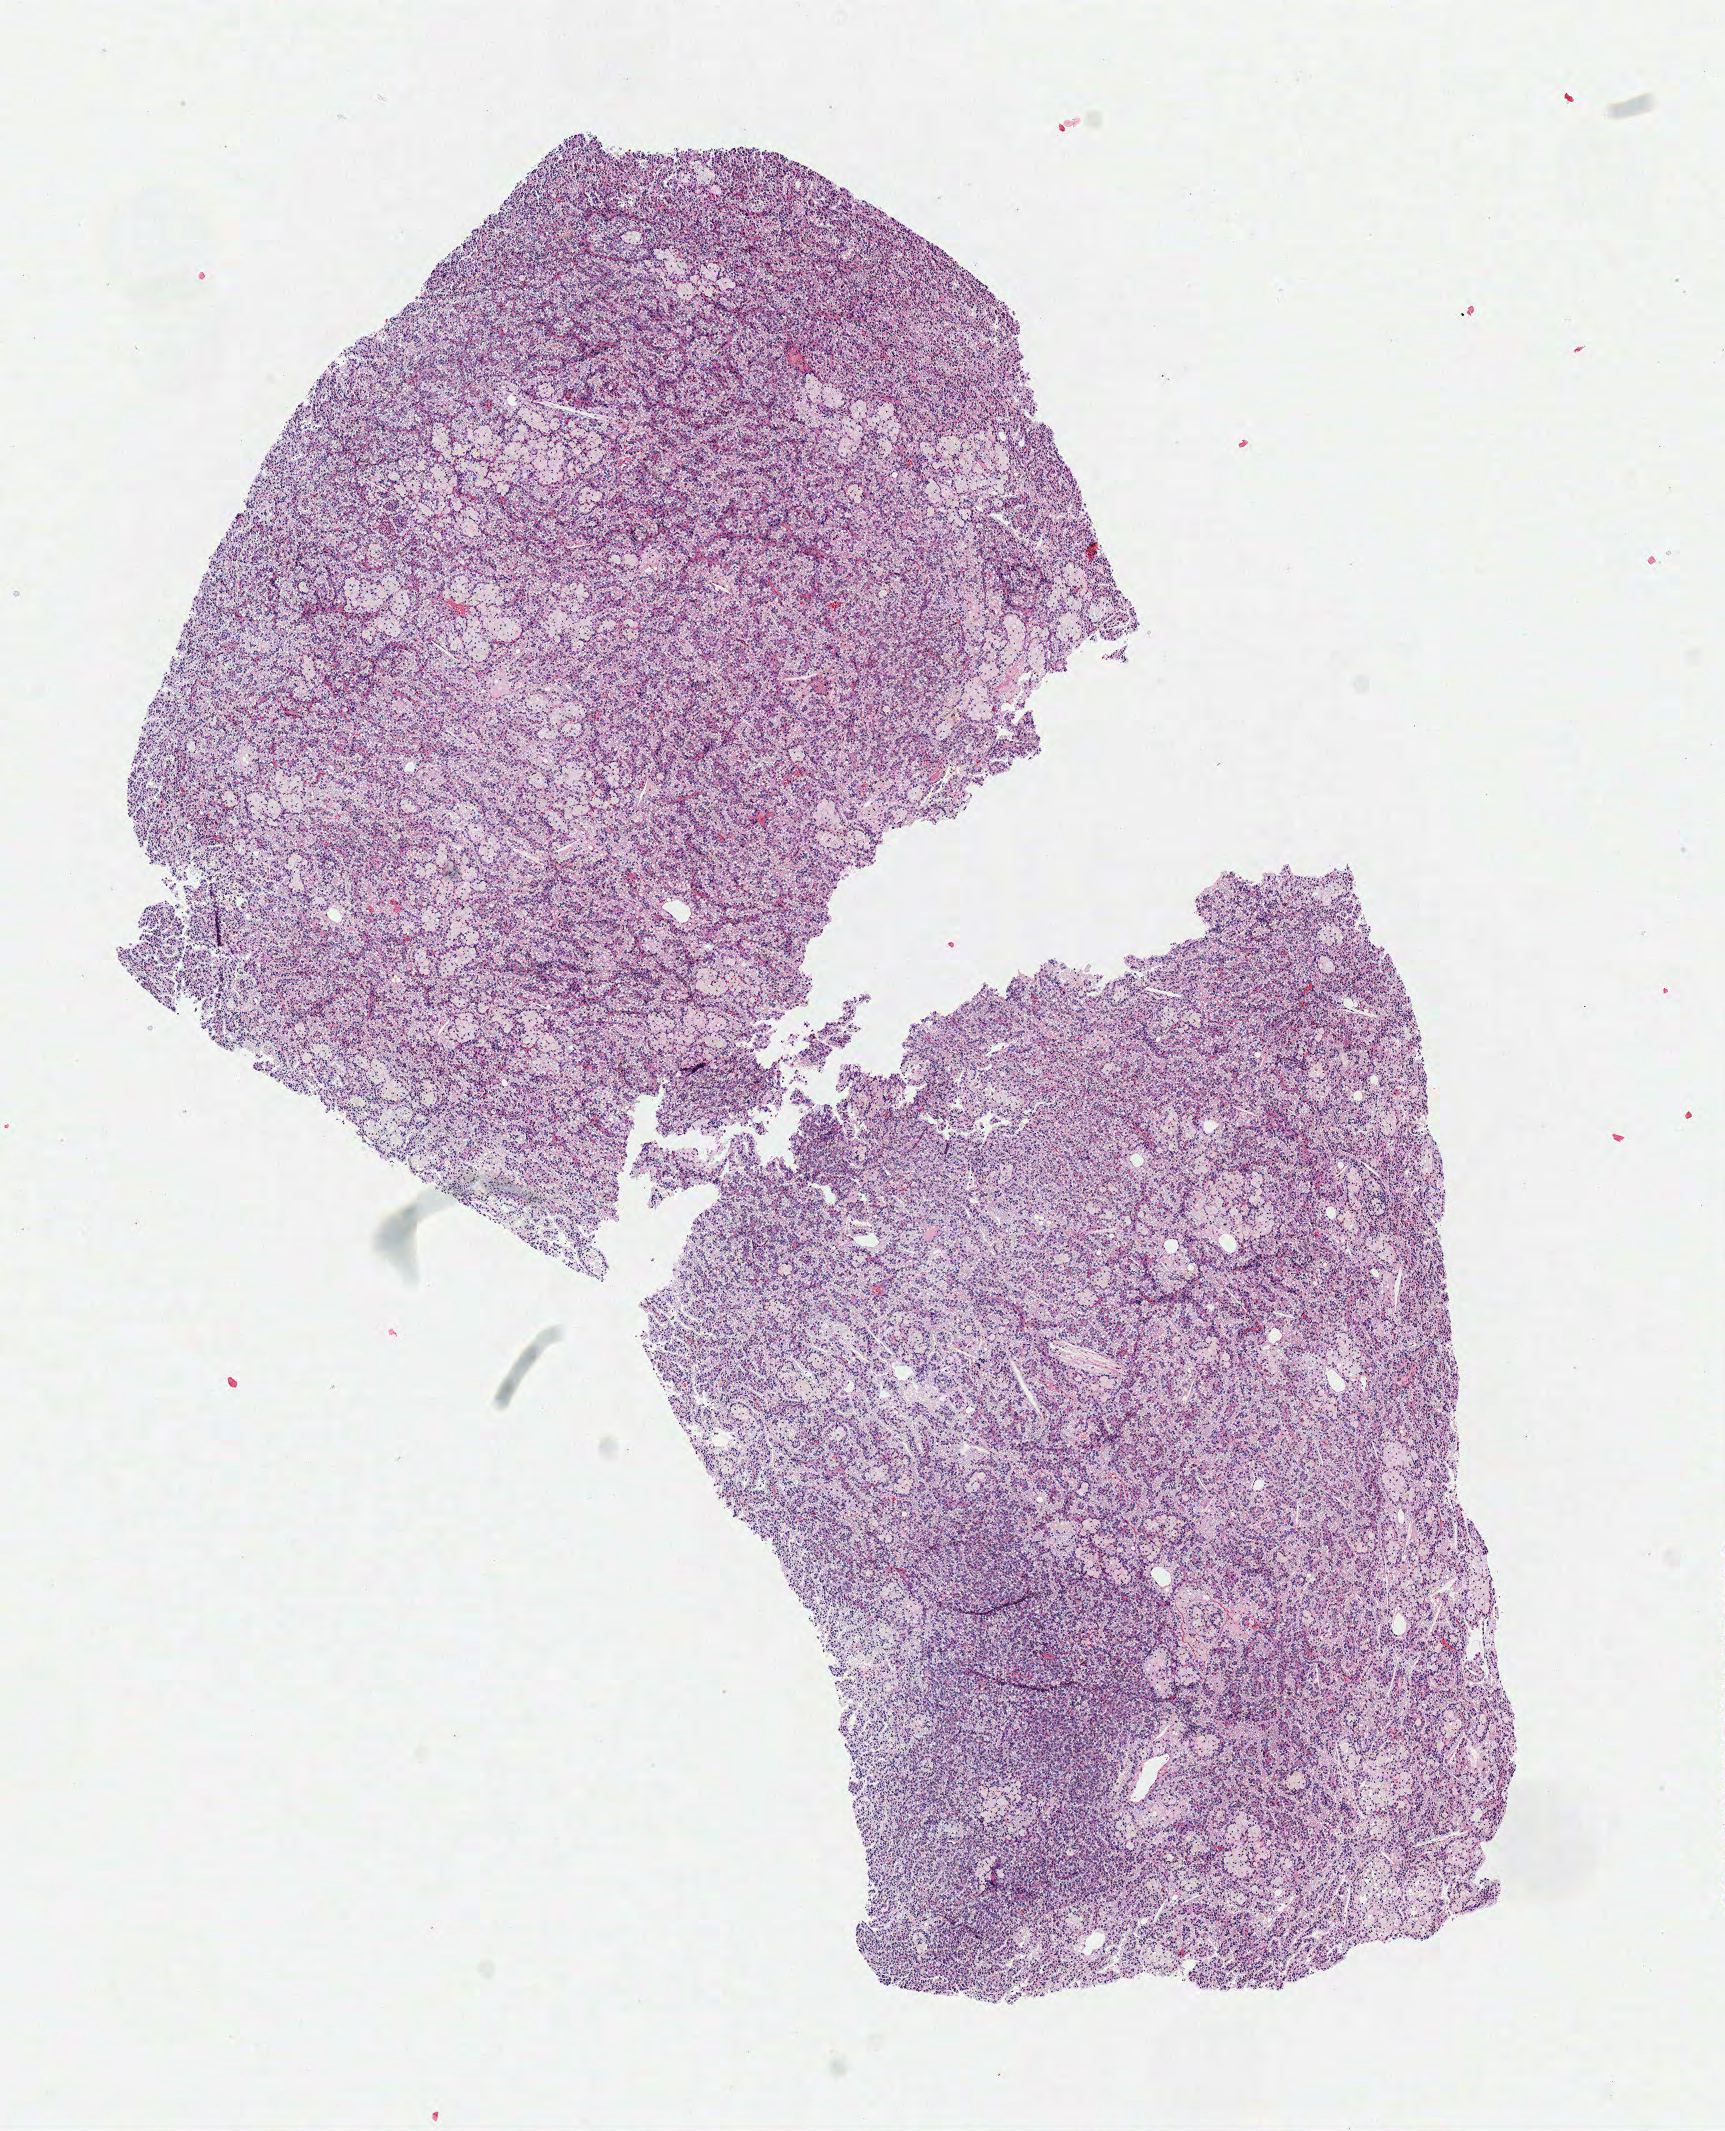
H&E-stained whole-slide image — a low-resolution overview of the entire scanned area, about 6.8 x 8.4 mm (acquisition: 40x scan). Frozen section from the top of the tissue portion. Kidney, primary tumour sample. Male, age 57 years at initial diagnosis. Slide review estimates, as recorded: tumour cells 95%, tumour nuclei 78%, normal cells 0%, stromal cells 5%, necrosis 0%. Infiltration values recorded for this section: lymphocyte infiltration 3%, monocyte infiltration 15%, neutrophil infiltration 0%.
* AJCC pathologic stage: I
* laterality: left
* pathologic diagnosis: Papillary adenocarcinoma, NOS